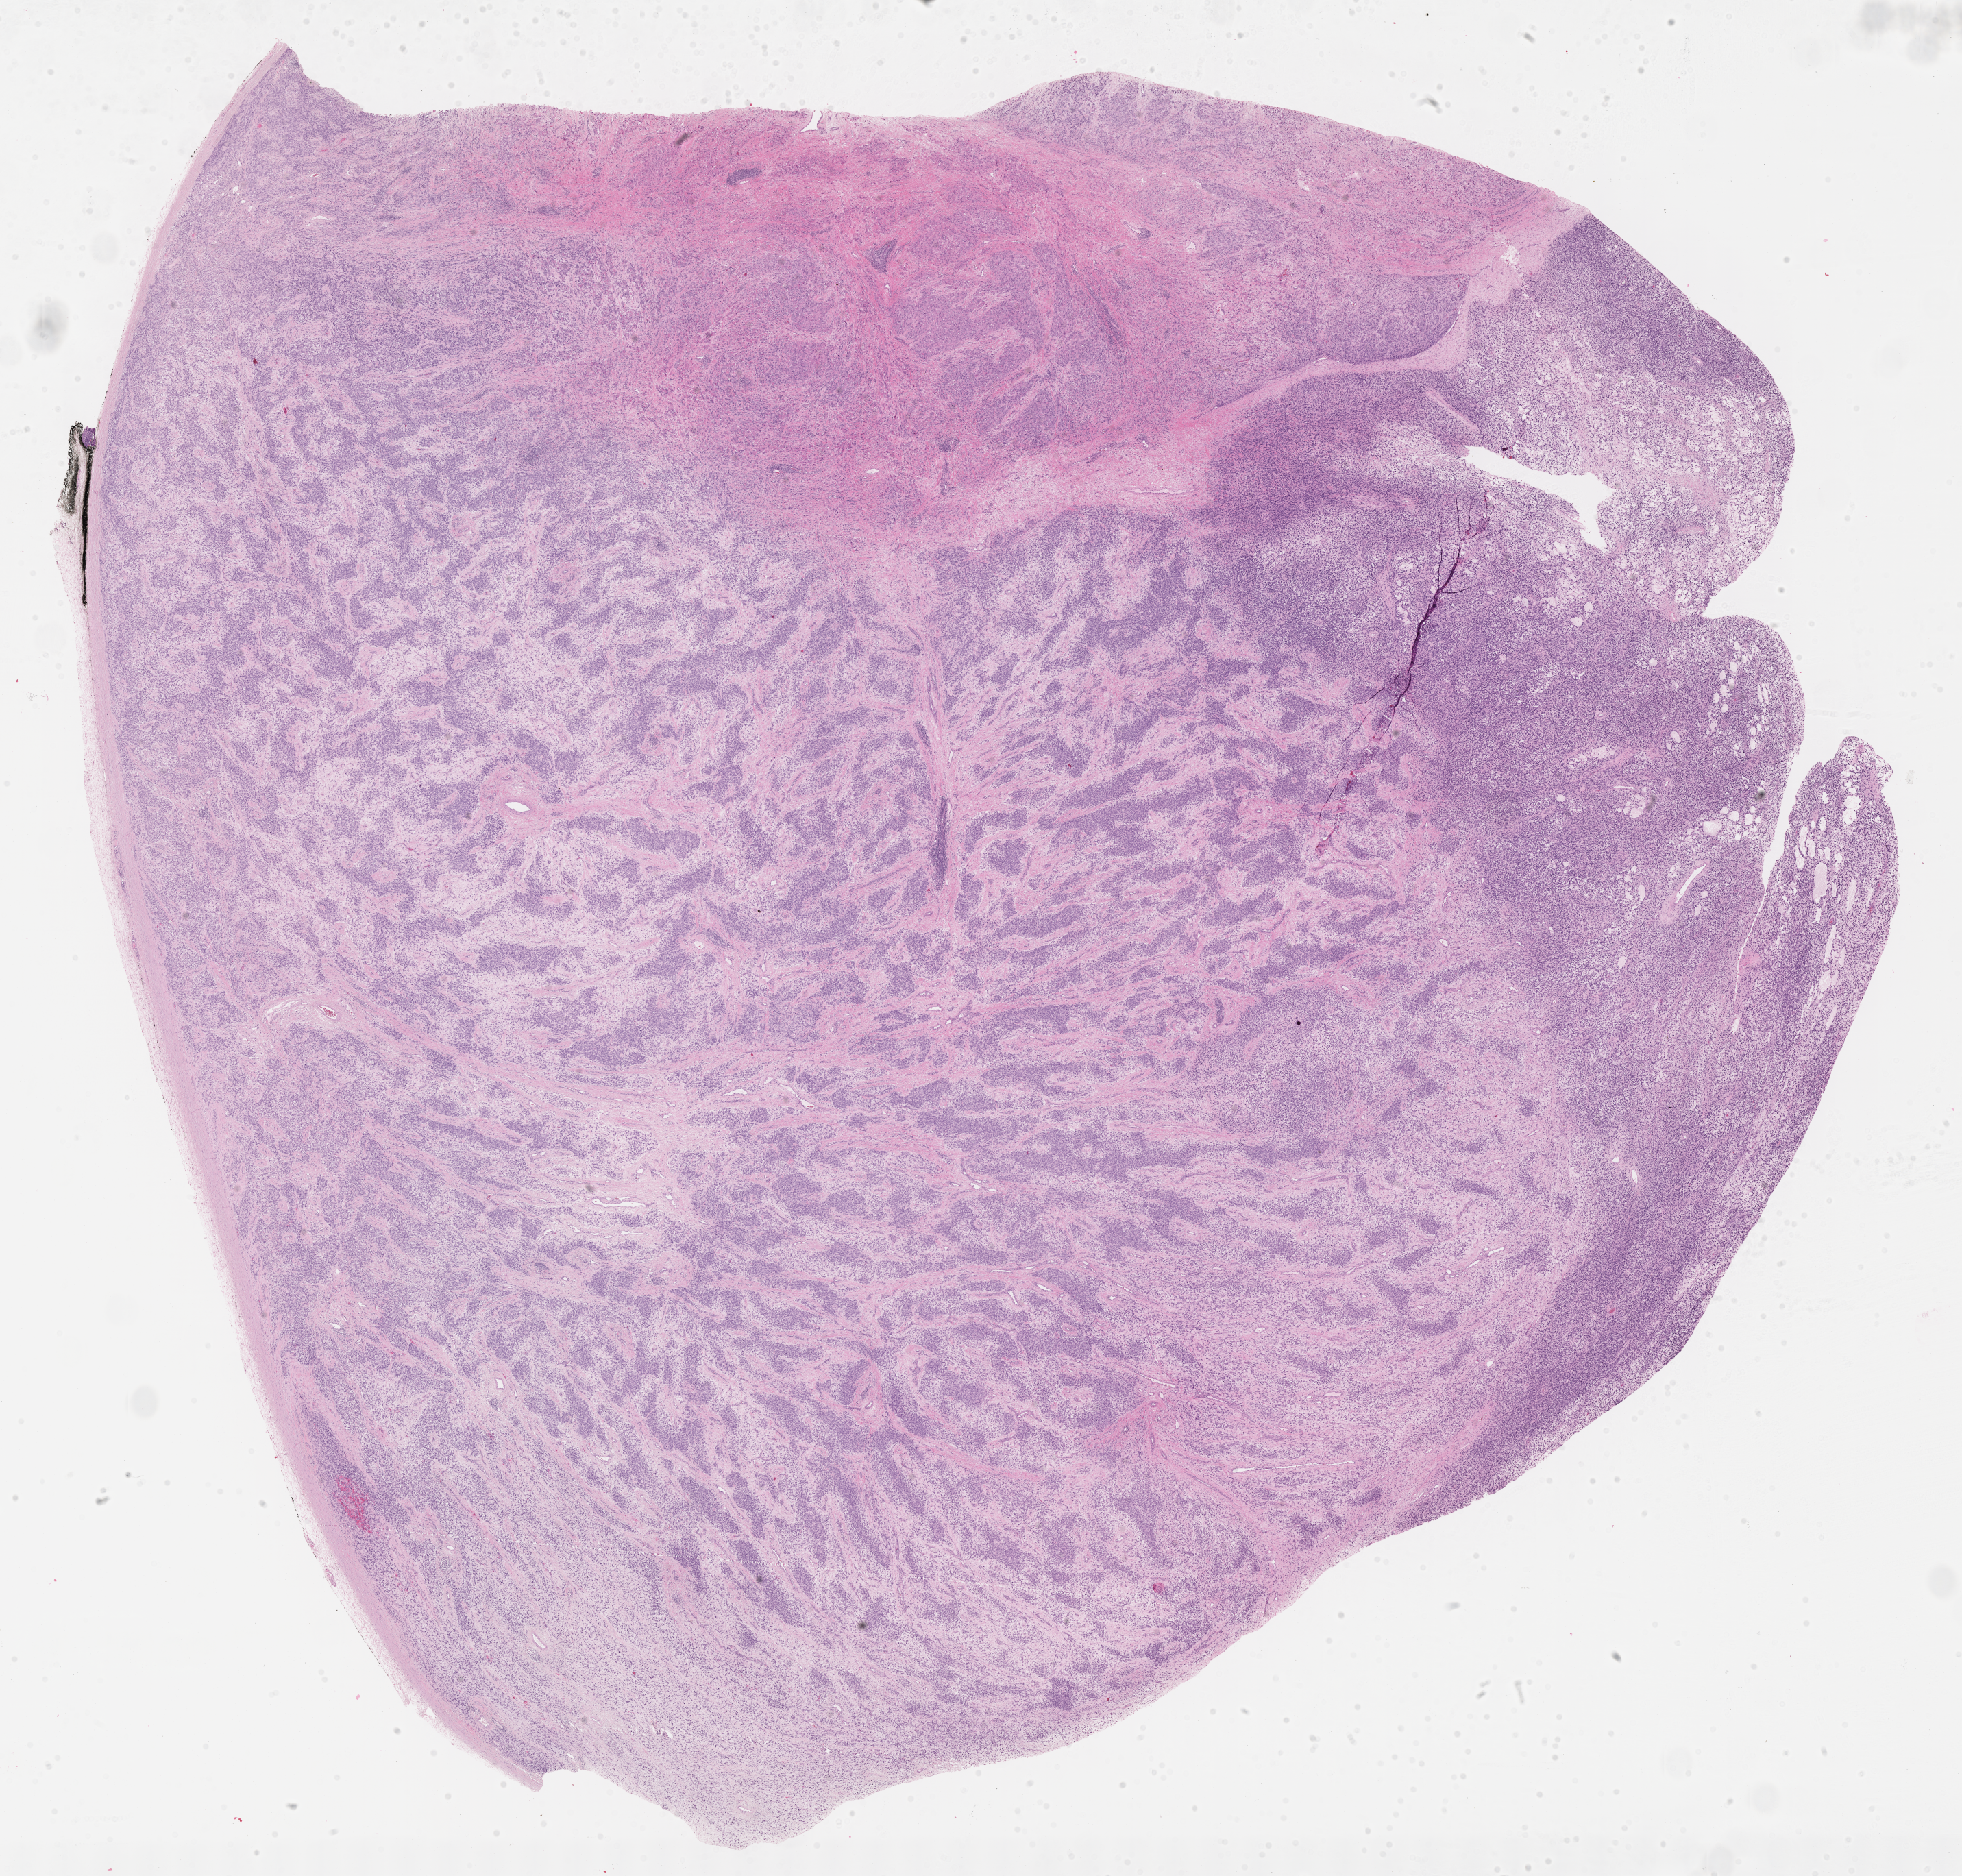
Hematoxylin and eosin (H&E) whole-slide image of tumor tissue — shown as a low-resolution overview of the whole scanned area (about 23.1 x 22.1 mm); formalin-fixed, paraffin-embedded (FFPE) tissue; sample anatomic site: testicle, right. Male patient, age at diagnosis 10.3 years.
Diagnosis: rhabdomyosarcoma; histological classification: embryonal rhabdomyosarcoma.